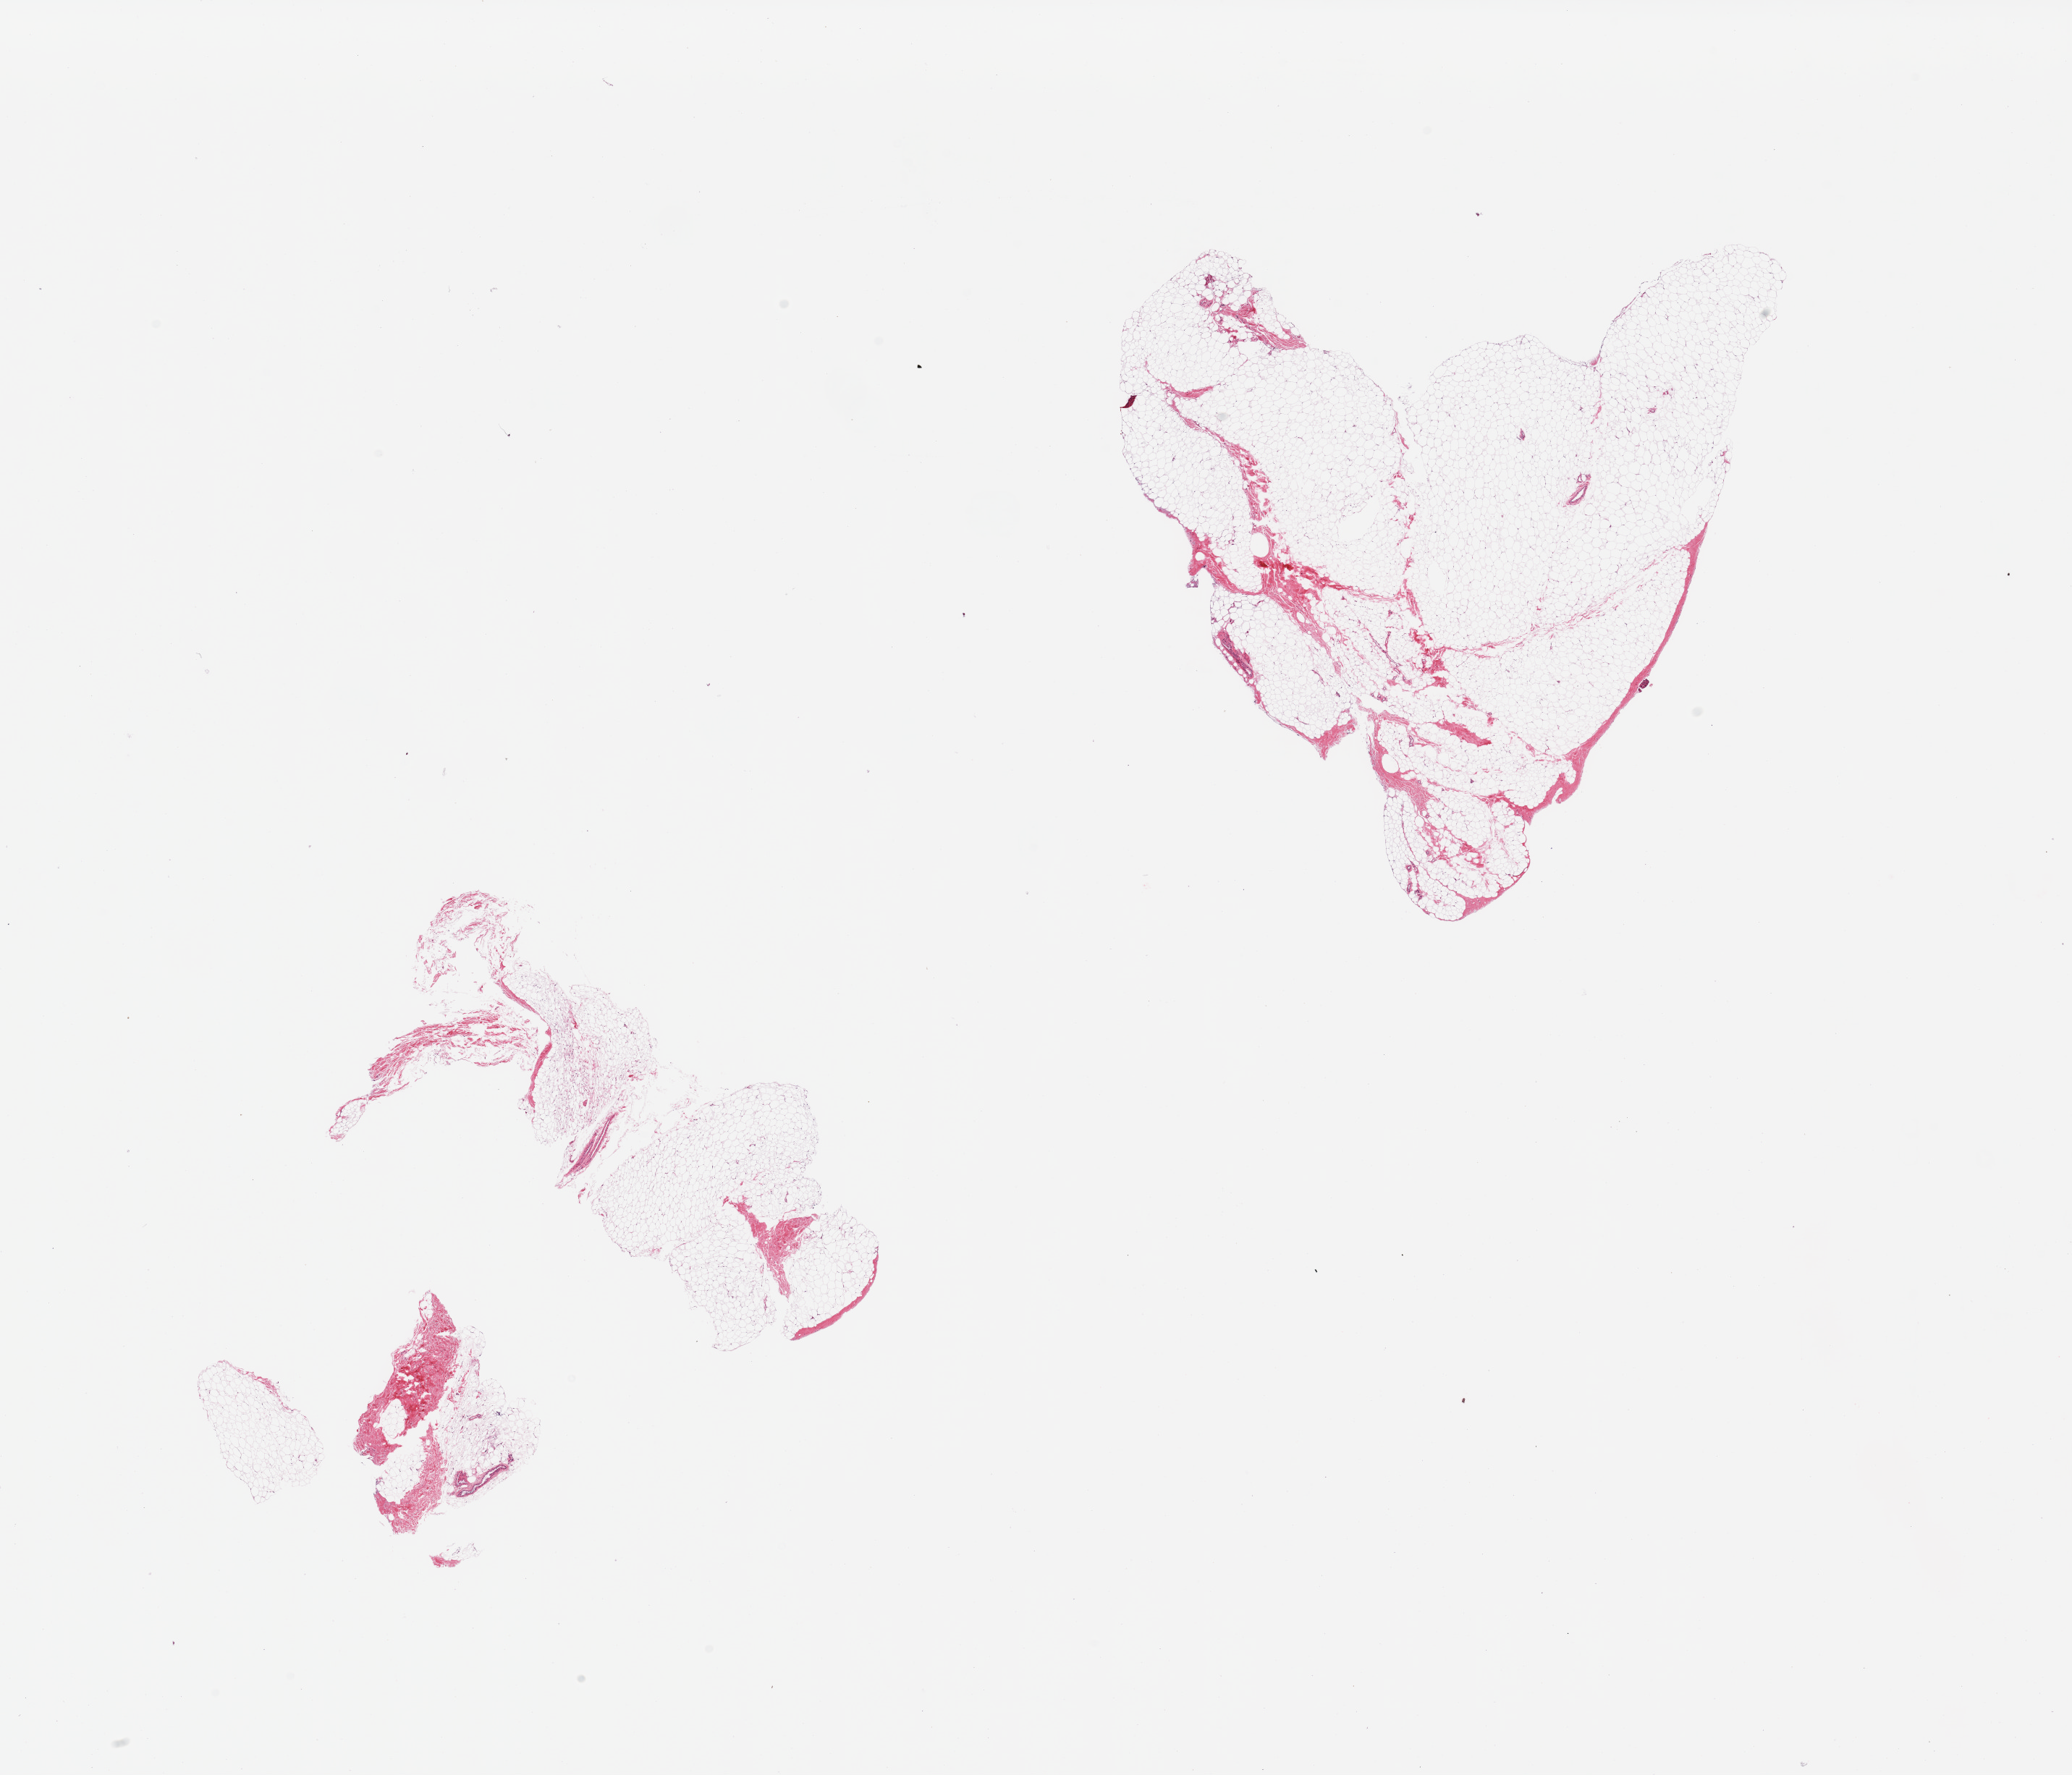
H&E whole-slide image, brightfield — low-resolution overview of the scanned area, about 22.6 x 19.4 mm. PAXgene-fixed paraffin-embedded (PFPE) section. Target tissue: breast. Tissue donor sample. Donor sex: male.
Reviewer comment on this tissue sample: 2 pieces; fibroadipose tissue with no mammary ducts.